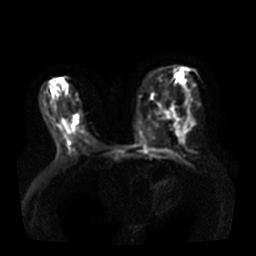
Breast MRI, one axial slice. Slice 17 of 36 in the series (ordered by position). Diffusion-weighted series; image 2 of 4 stored at this slice position (different b-values; order by instance number). 3 T. 5 mm slice thickness. 256 × 256 image matrix, field of view 360 × 360 mm. Female patient.
Structures marked on this image (manually delineated by an expert):
- tumour on diffusion-weighted imaging: bounding box [x1, y1, x2, y2] px = [74, 117, 78, 124]